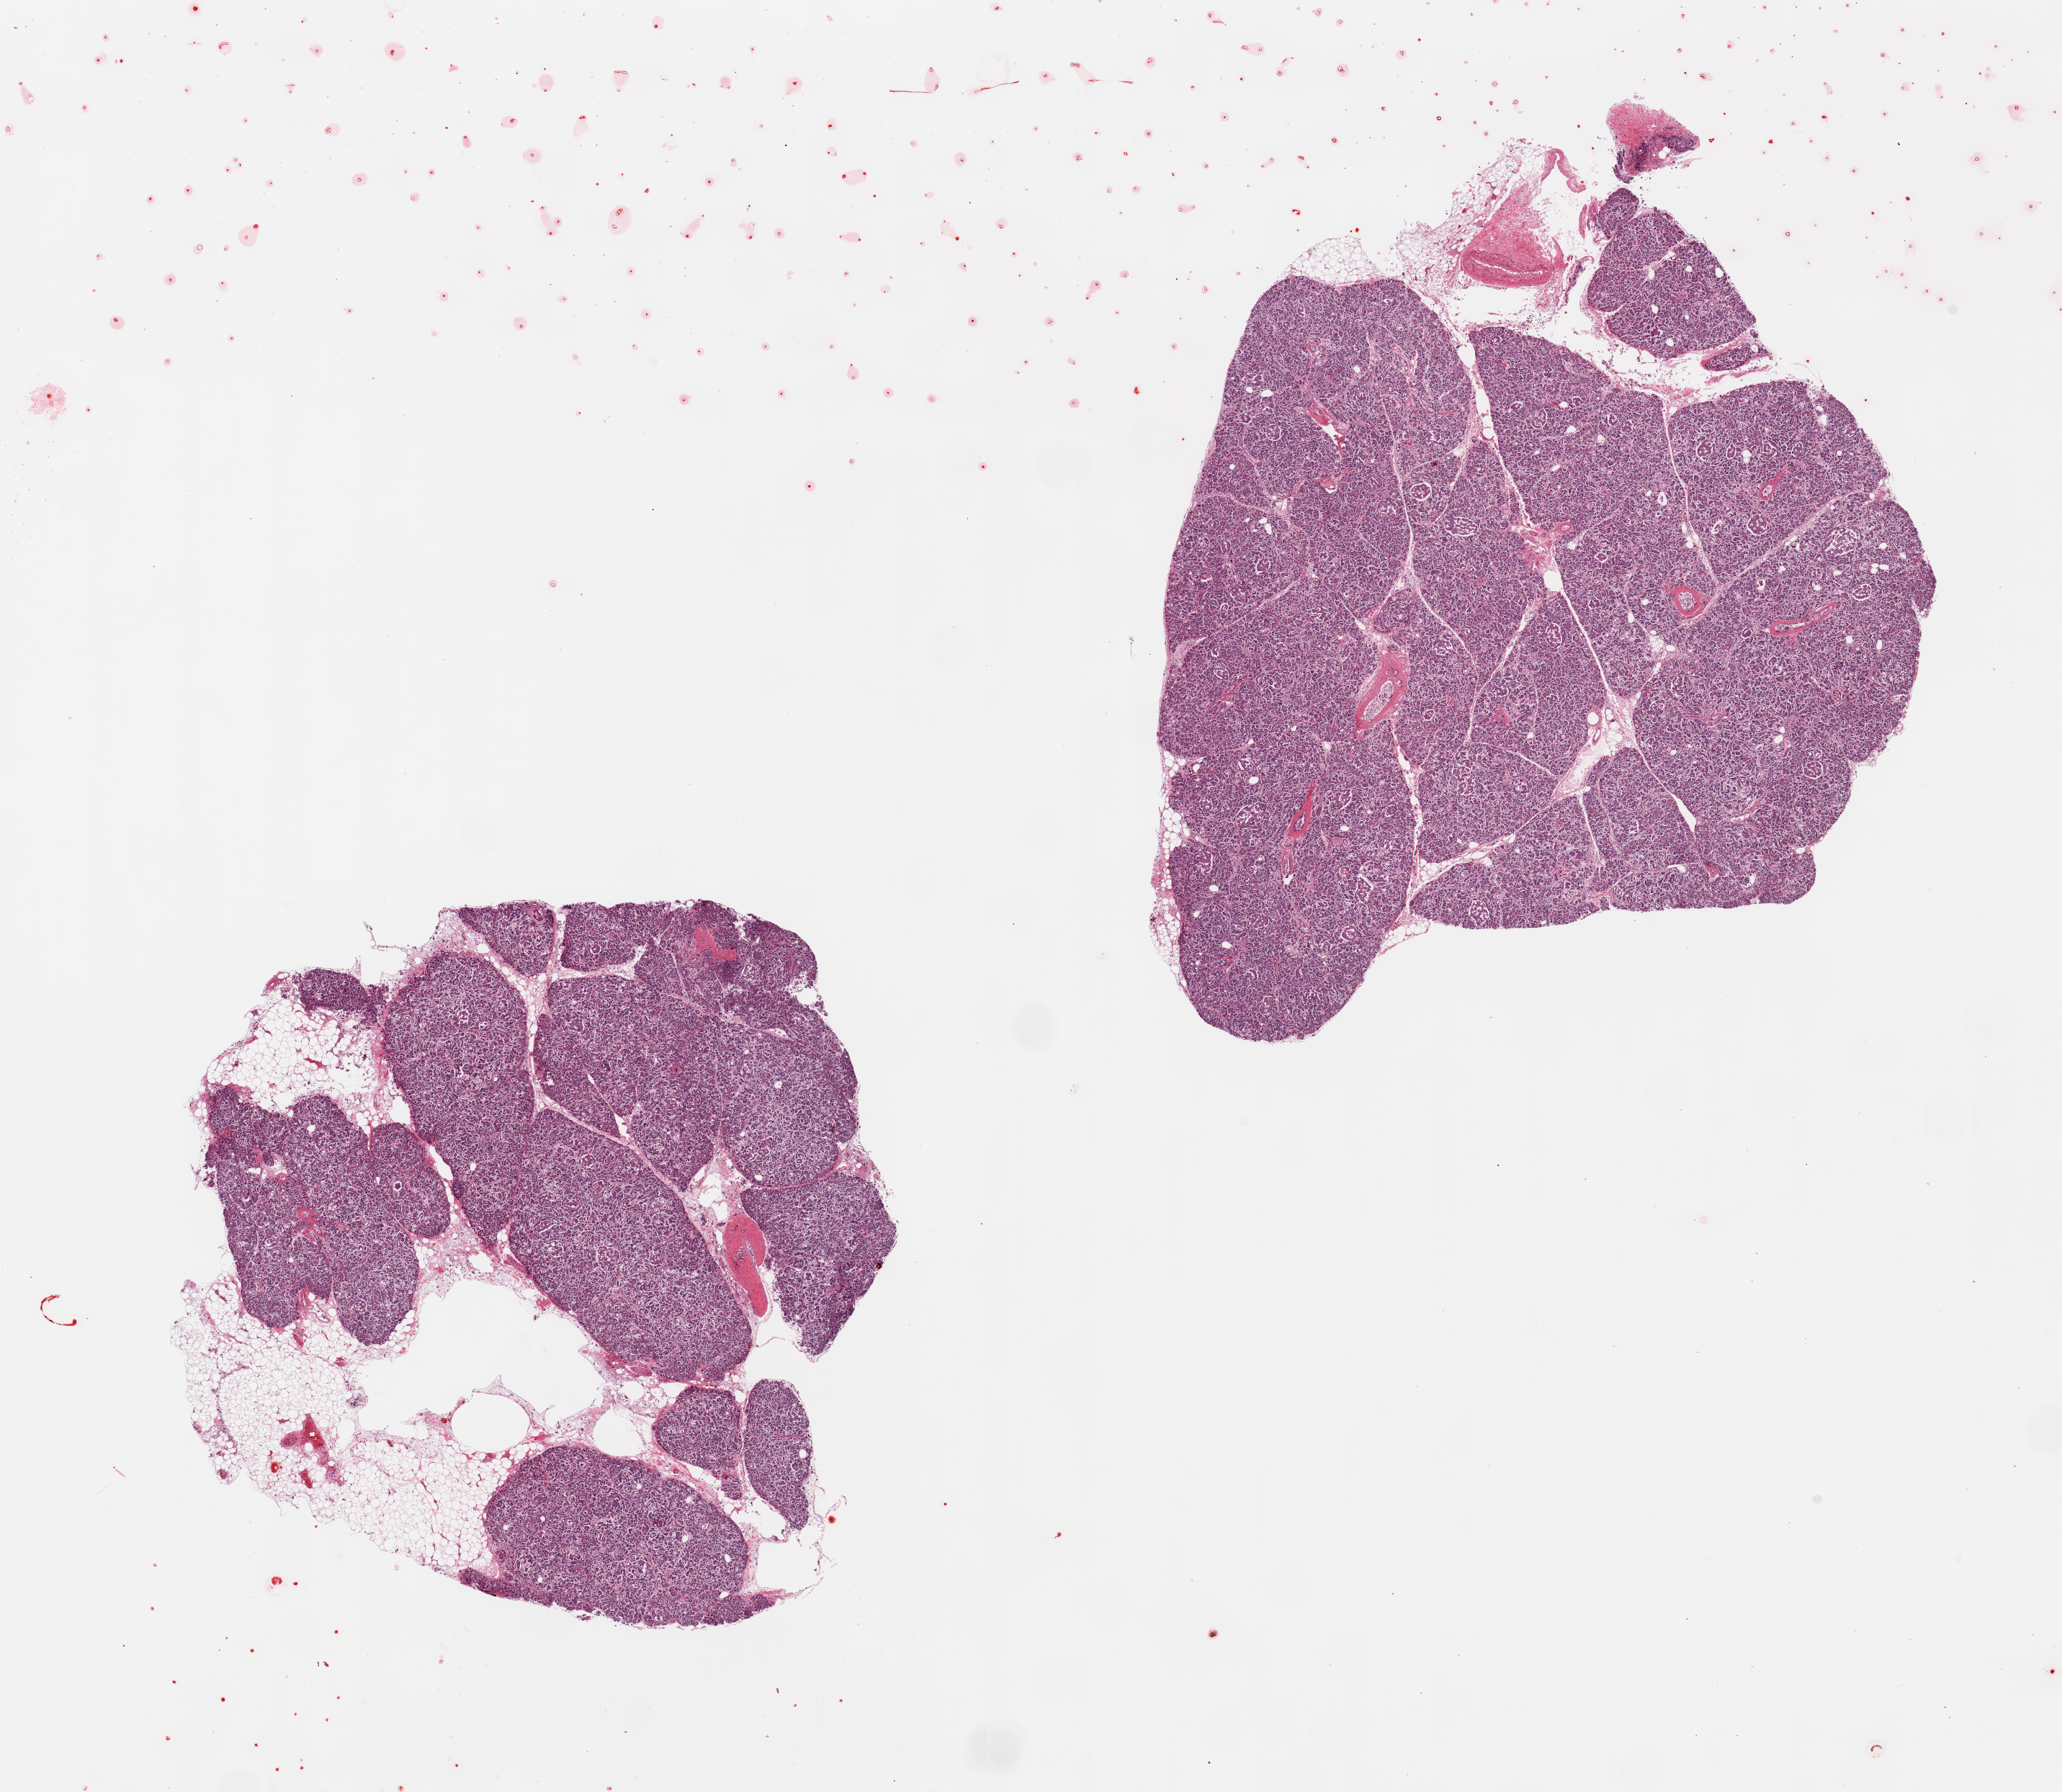
Whole-slide image, H&E stain, brightfield — shown as a low-resolution overview of the whole scanned area (about 22.6 x 19.7 mm); PAXgene-fixed paraffin-embedded (PFPE) section; section of pancreas (target tissue); donor tissue sample. Donor sex: female.
Reviewer comment on this tissue sample: 2 pieces; 30% internal and external fat; islets not reduced in number.